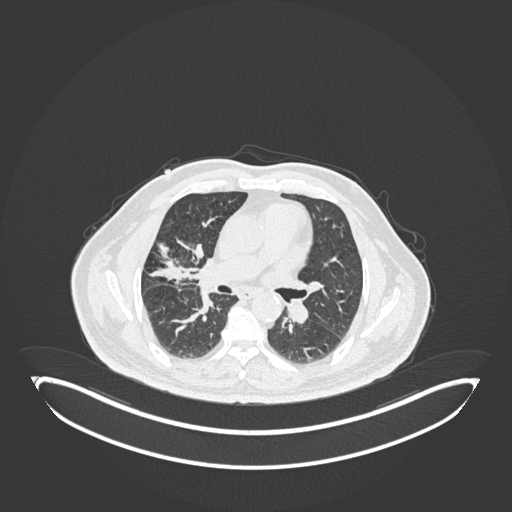
Chest CT, one axial slice. Position 89 of 247 along the scan axis. Reconstruction kernel B30f. Lung window (W 1500 / L -600 HU). 1 mm slice thickness. 512 × 512 image matrix, field of view 500 × 500 mm. Male patient, age 72 years. From the clinical record (not read from this slice): clinical TNM (as recorded): T1c N0 M0.
Structures marked on this image (rectangle marked by the reading radiologist):
- lung tumour (recorded histology: squamous cell carcinoma): bounding box [x1, y1, x2, y2] px = [187, 236, 218, 299]